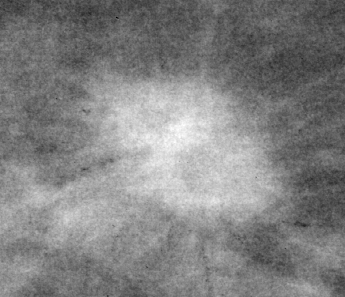
Region of interest cut from a scanned film mammogram (one marked finding), right breast, MLO view.
Marked abnormality: mass, shape oval, margins spiculated; BI-RADS assessment category 5; pathology (as recorded): malignant.